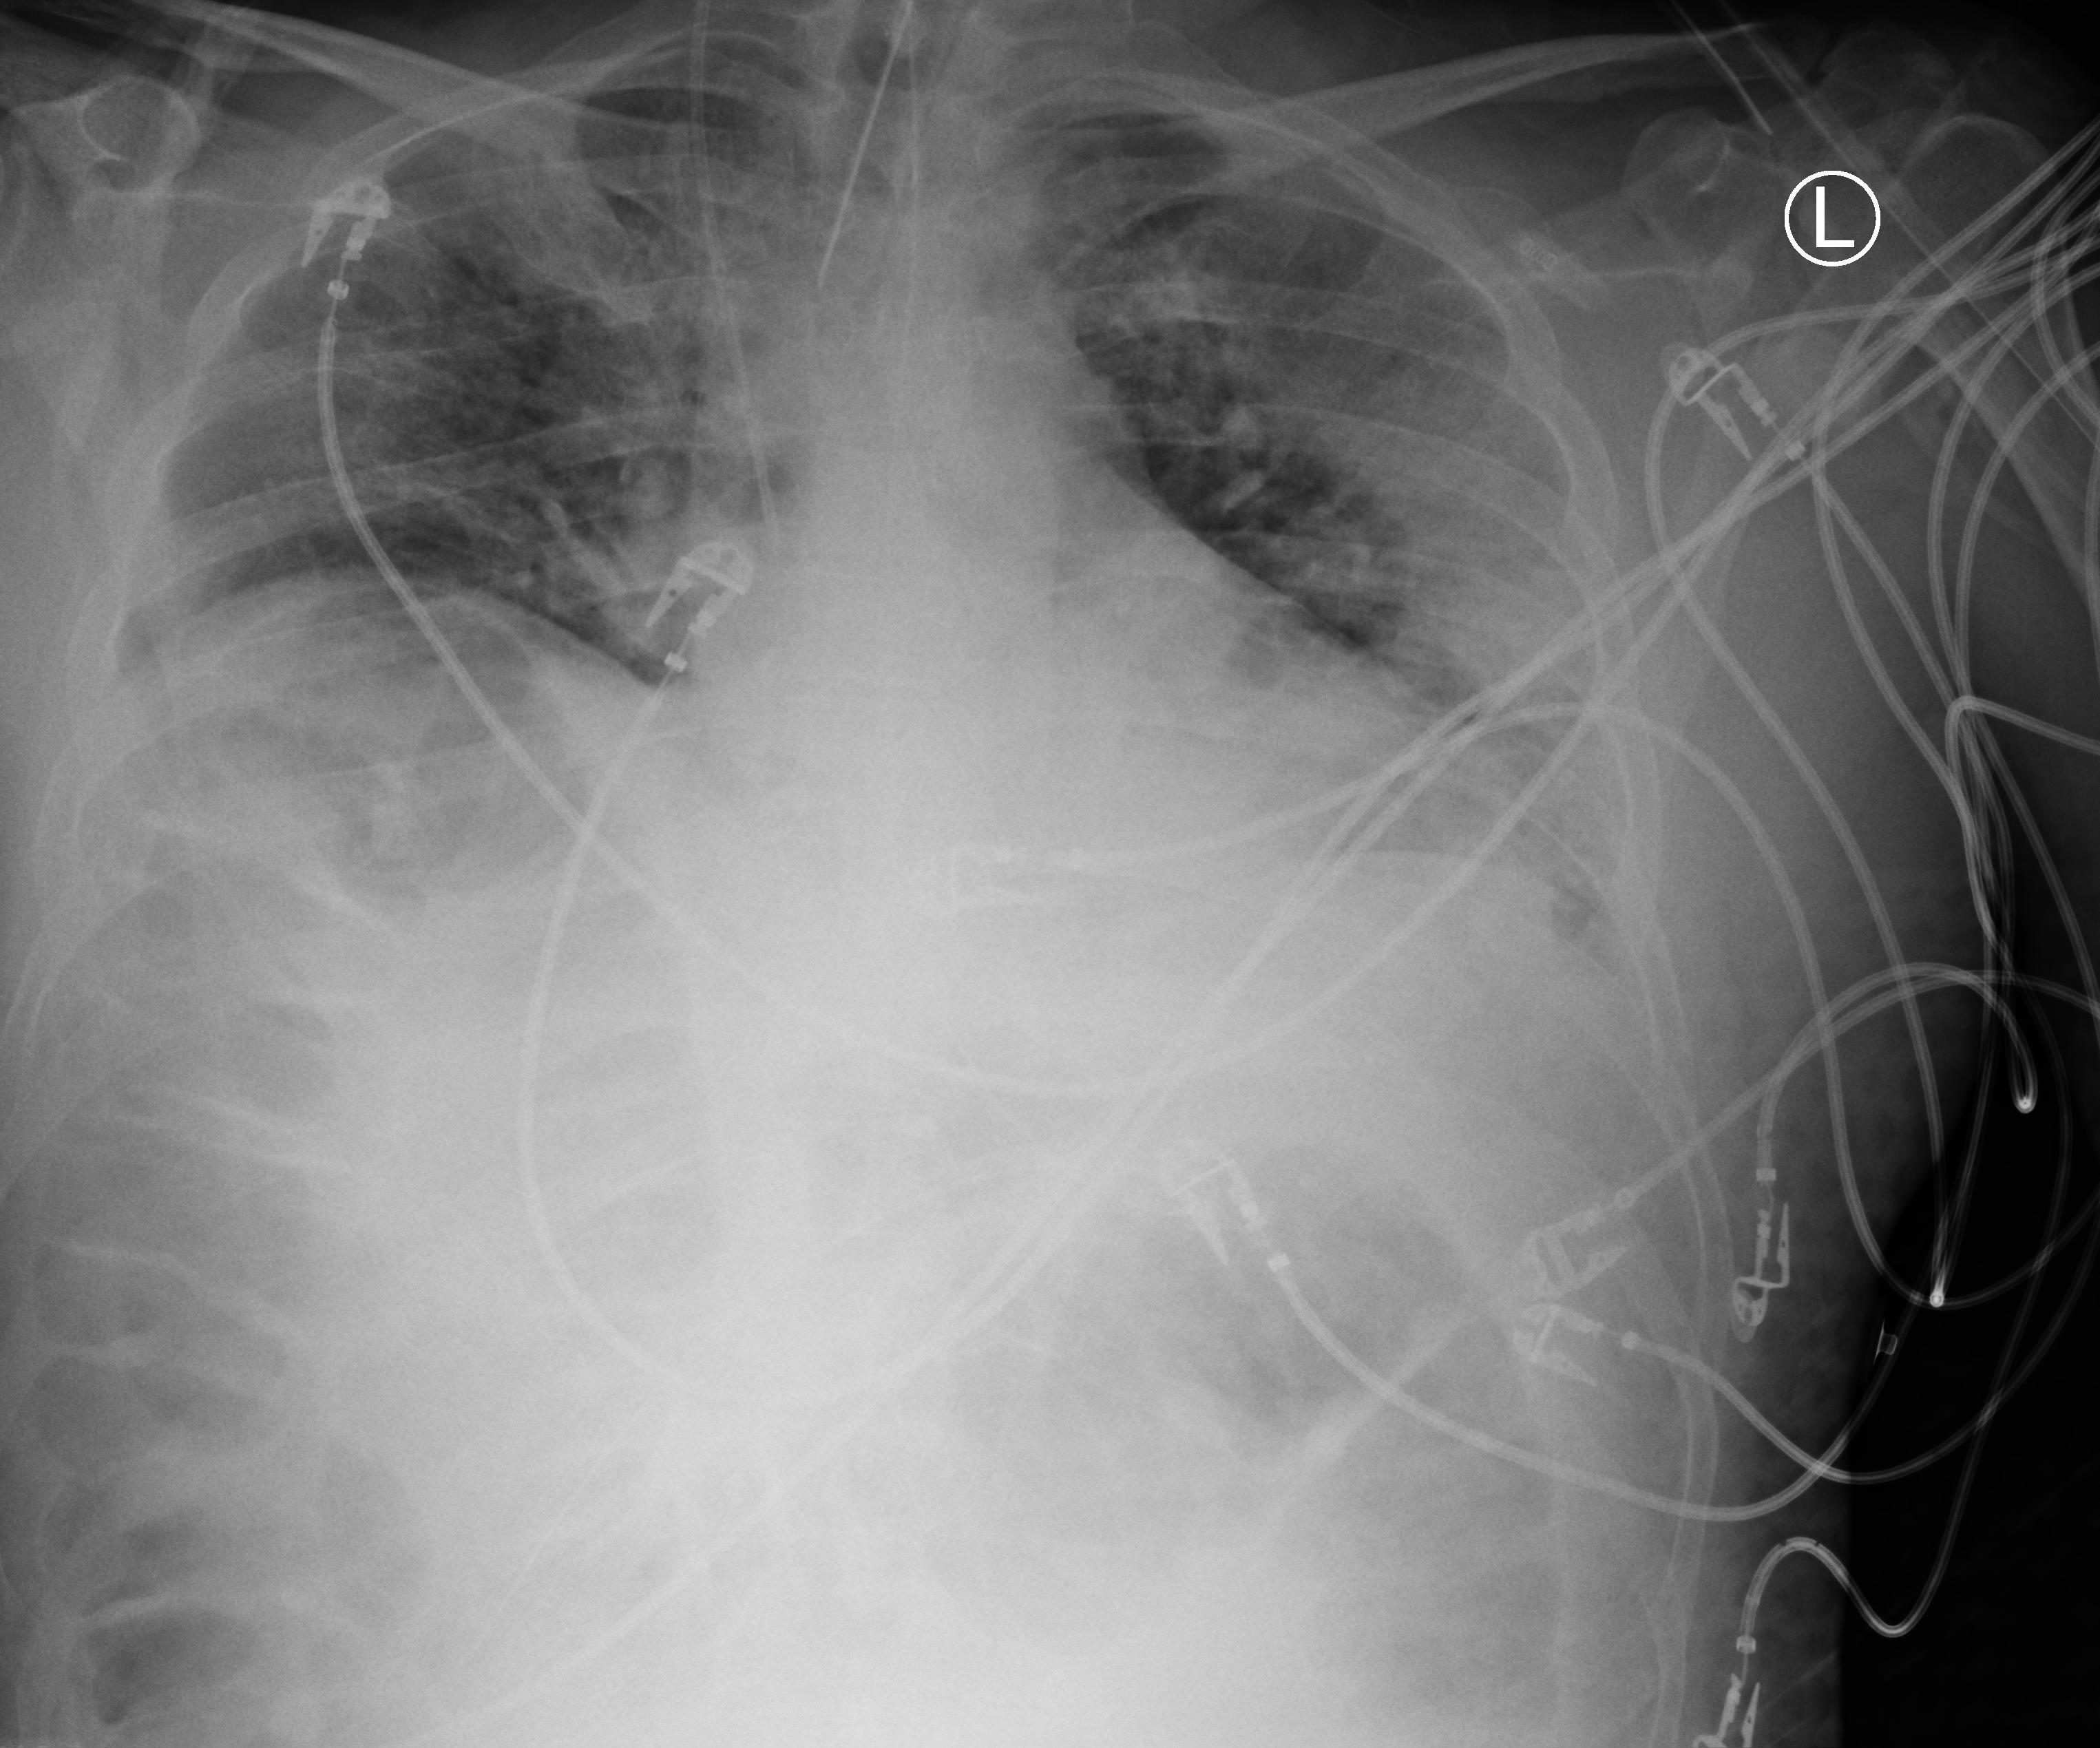
Bedside chest radiograph (computed radiography); anteroposterior (AP) projection. Patient hospitalised with COVID-19; male, aged 18–59 years.
Admission-level facts for this patient (not findings on this image; timing relative to this image not recorded): COPD (admission record): no; length of hospital stay: 48 days.